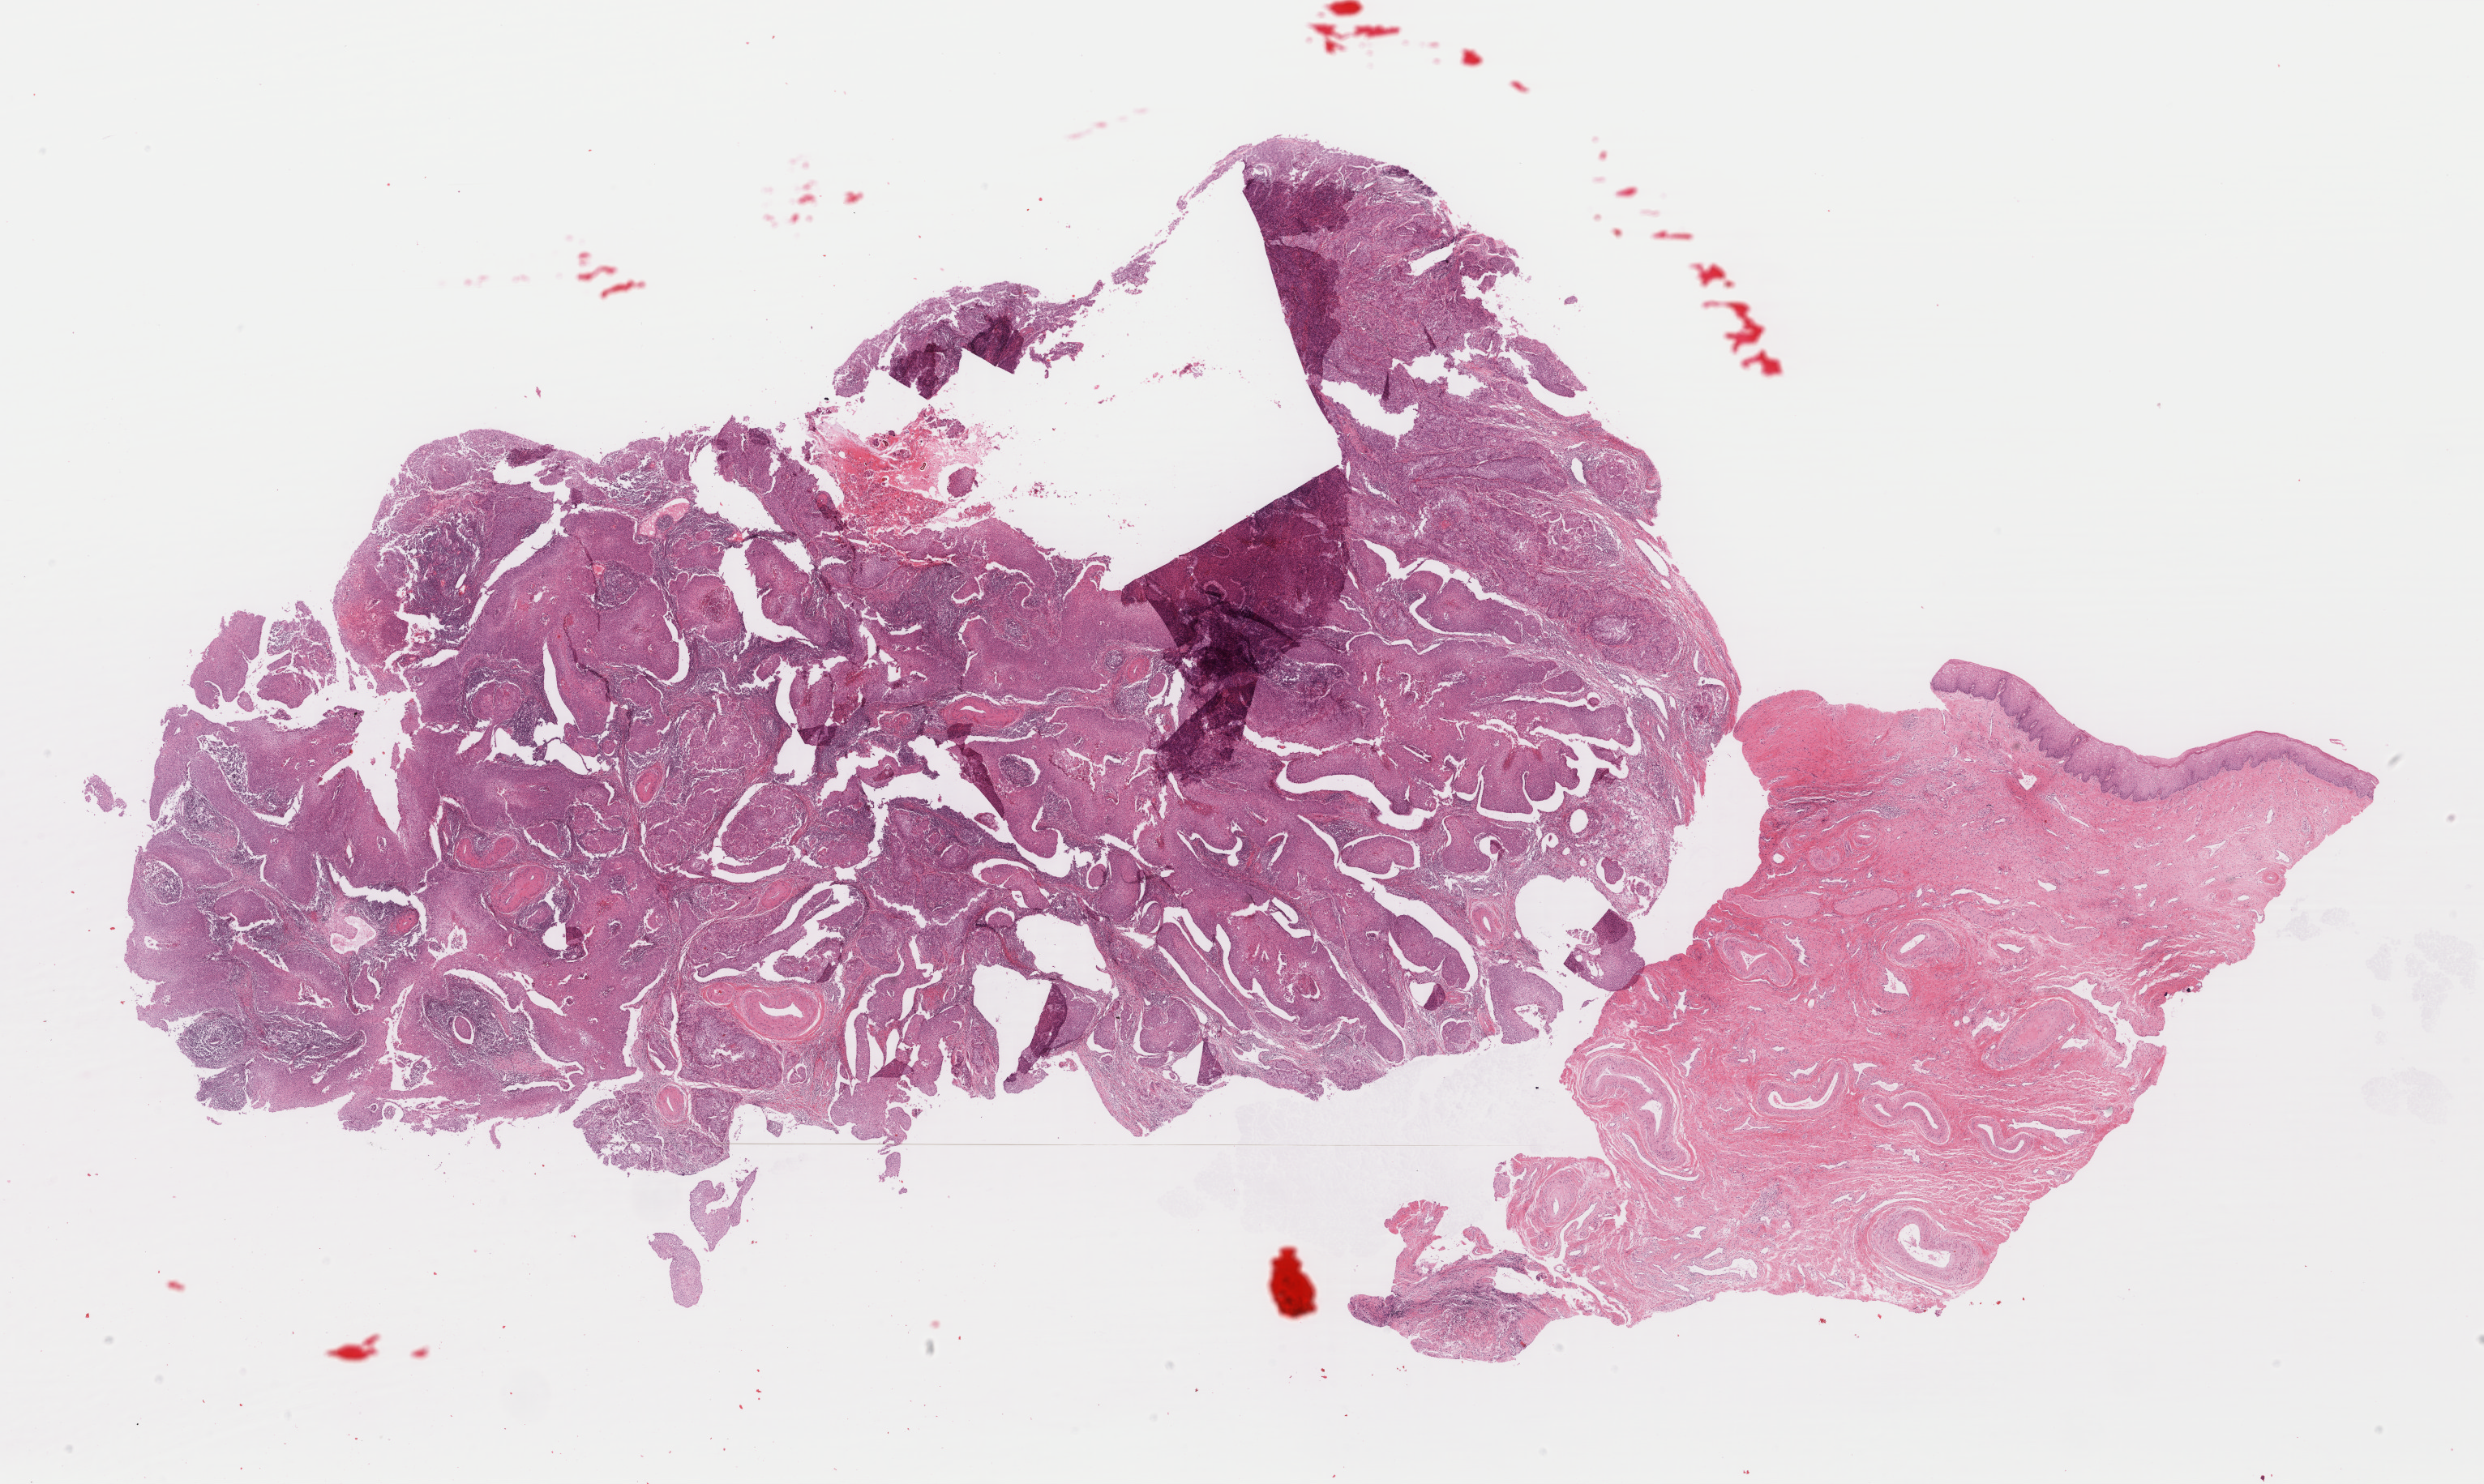
Hematoxylin and eosin (H&E) stained whole-slide image — whole scanned area (about 24.3 x 14.5 mm, acquisition: 40x scan) shown as a low-resolution overview, FFPE section, cervix, primary tumour sample. Patient: female, age at initial diagnosis 45 years. Histologic grade: G2 (moderately differentiated).
• FIGO stage: IB
• pathologic diagnosis: Squamous cell carcinoma, large cell, nonkeratinizing, NOS (cervix uteri)